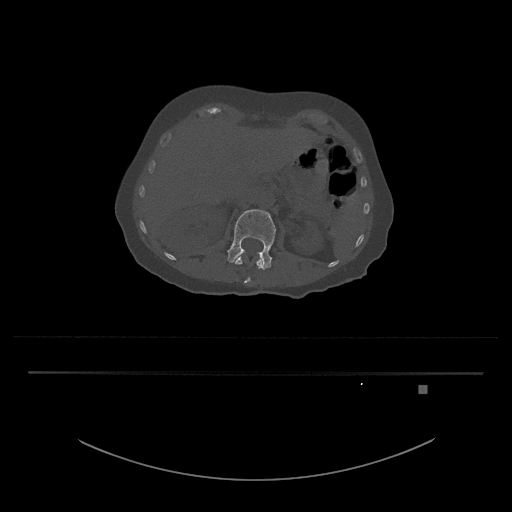
CT including the spine, one axial slice; position 512 of 797 along the scan axis; reconstruction kernel Br40s/3; 120 kVp; bone window (W 1800 / L 400 HU); 0.5 mm slice thickness; 512 × 512 image matrix. Female patient, age 57 years. Case-level facts recorded for this patient, not image findings: primary cancer: cervical.
Annotated regions visible in this slice (semi-automatic segmentation, software-assisted and operator-edited):
- L1 vertebra: bounding box [x1, y1, x2, y2] px = [235, 254, 264, 283]